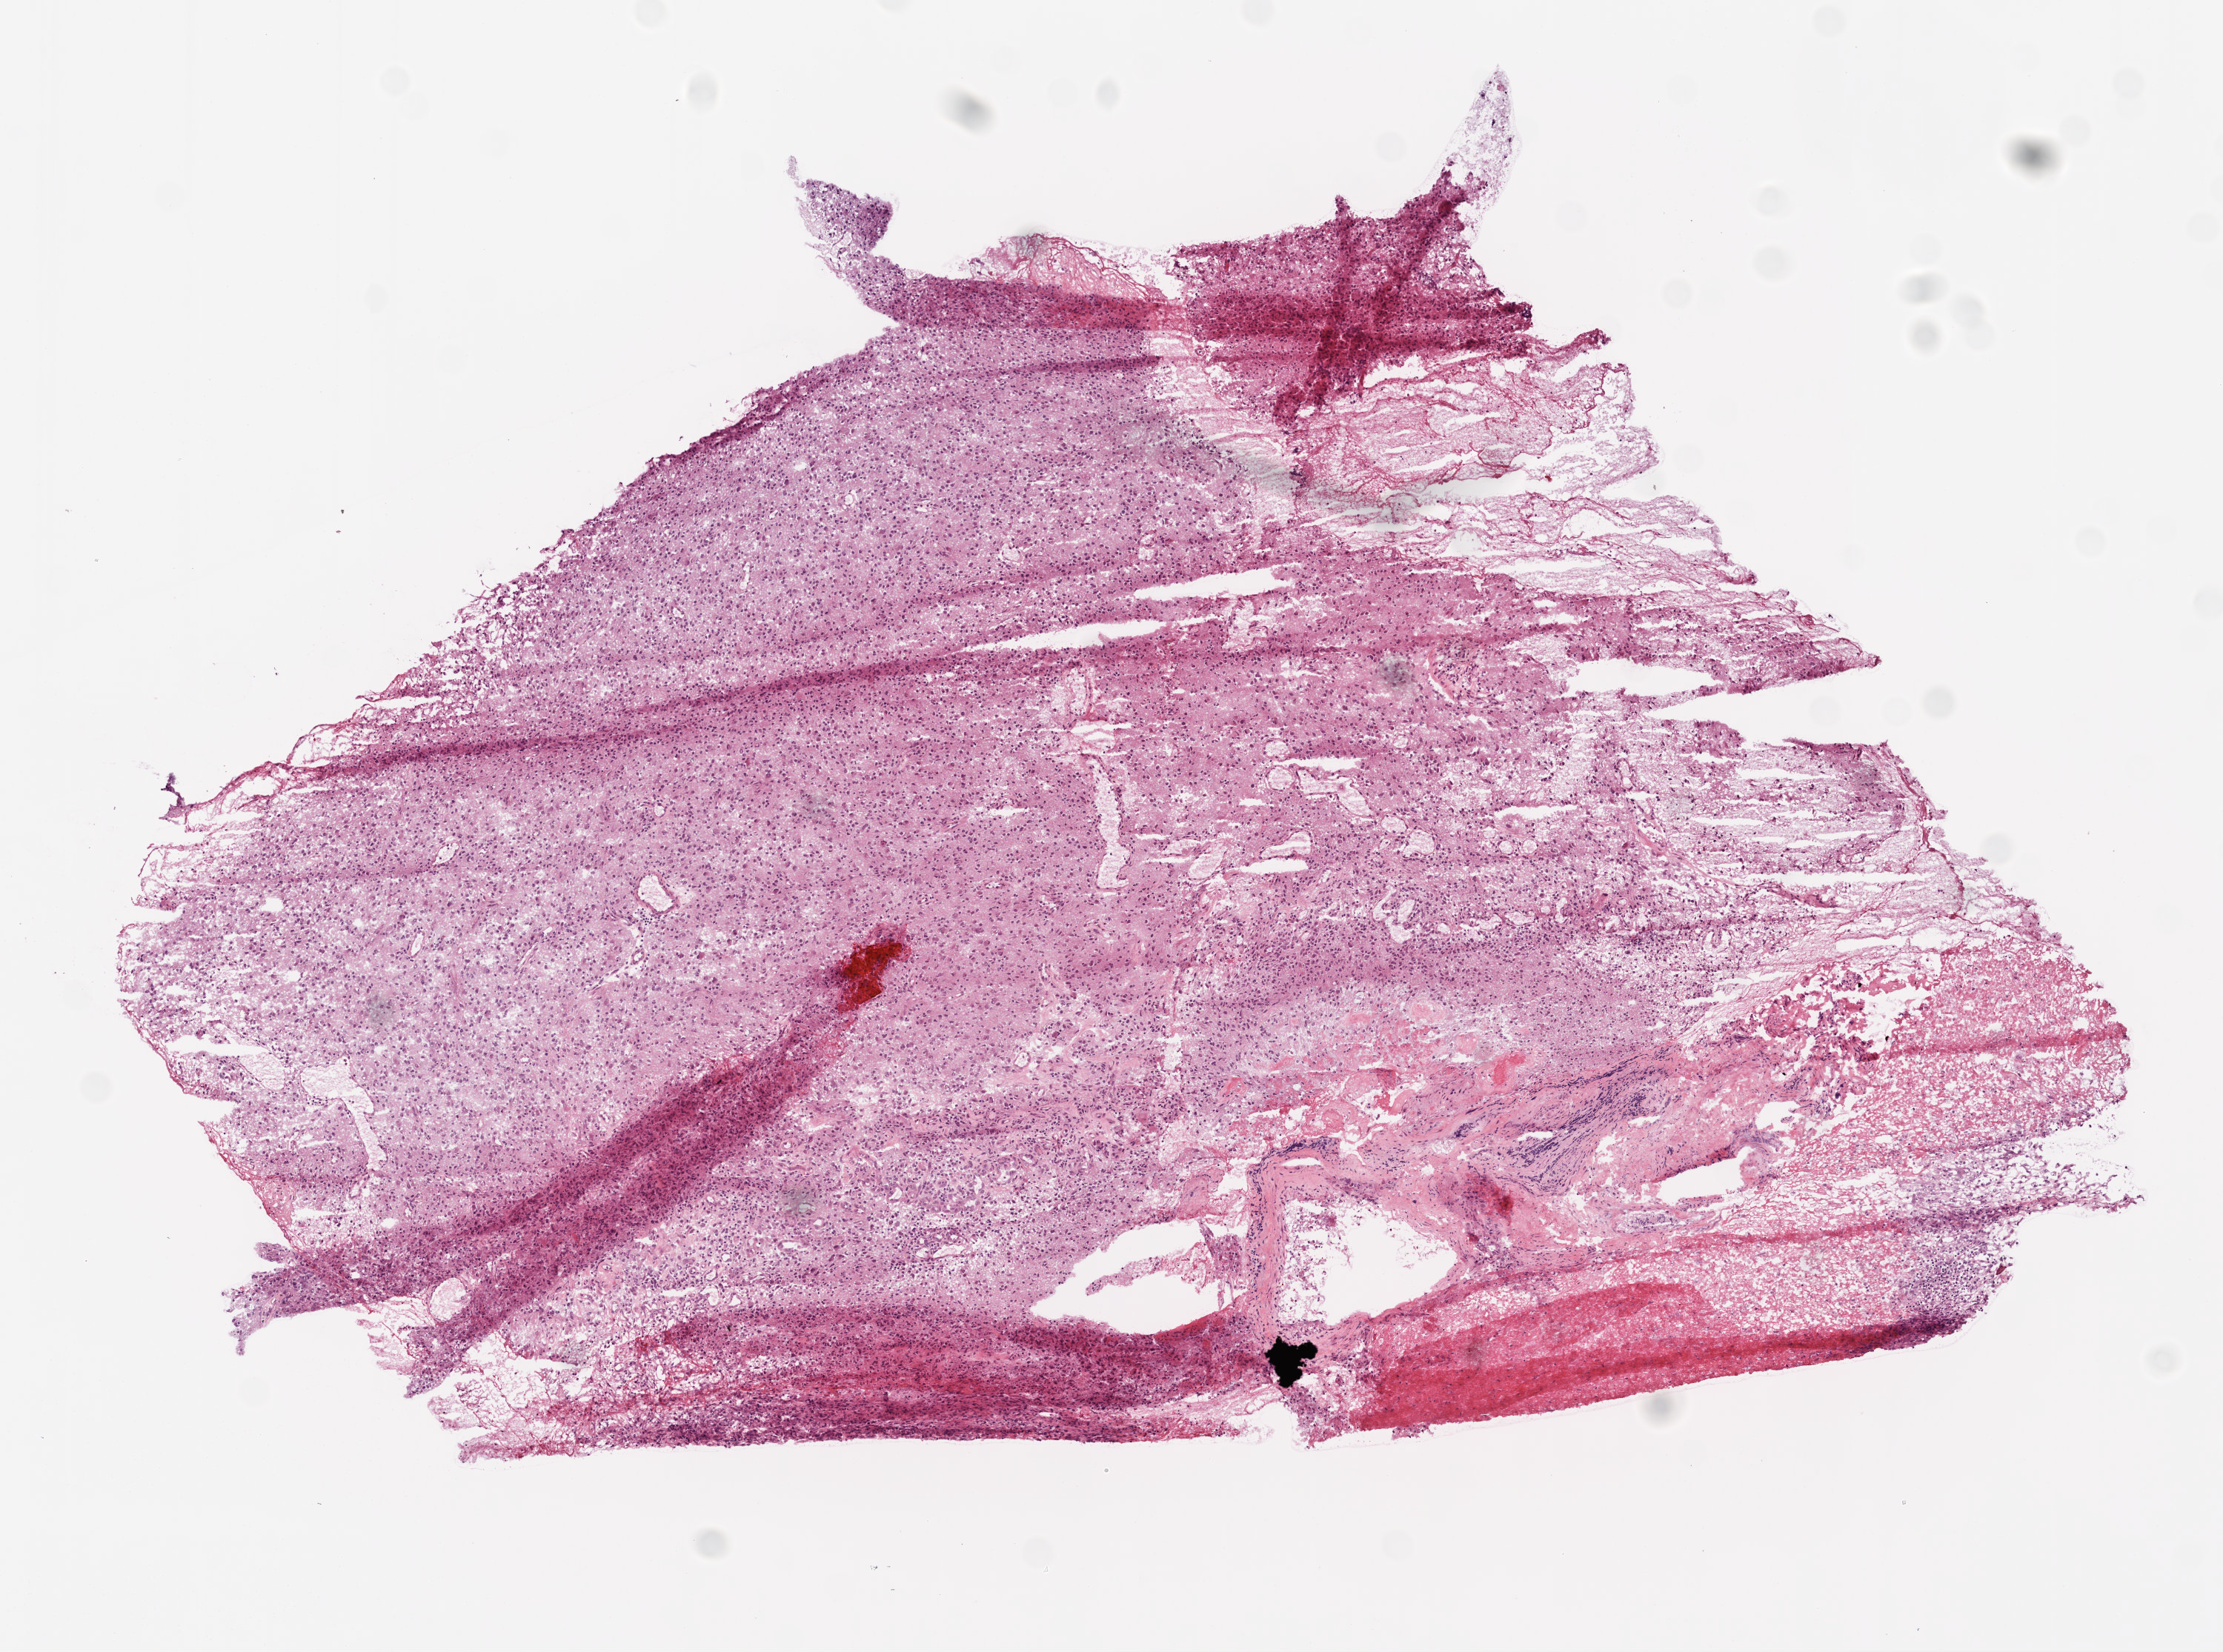
Hematoxylin and eosin (H&E) stained whole-slide image — low-resolution overview of the scanned area, about 6.0 x 4.5 mm (acquisition: 20x scan), frozen section from the top of the tissue portion, primary tumour sample from the brain. Patient: female, age at initial diagnosis 63 years. Pathologist review of this section (percent, as recorded): tumour cells 75%, tumour nuclei 90%, normal cells 0%, stromal cells 5%, necrosis 20%.
Pathologic diagnosis: Glioblastoma.